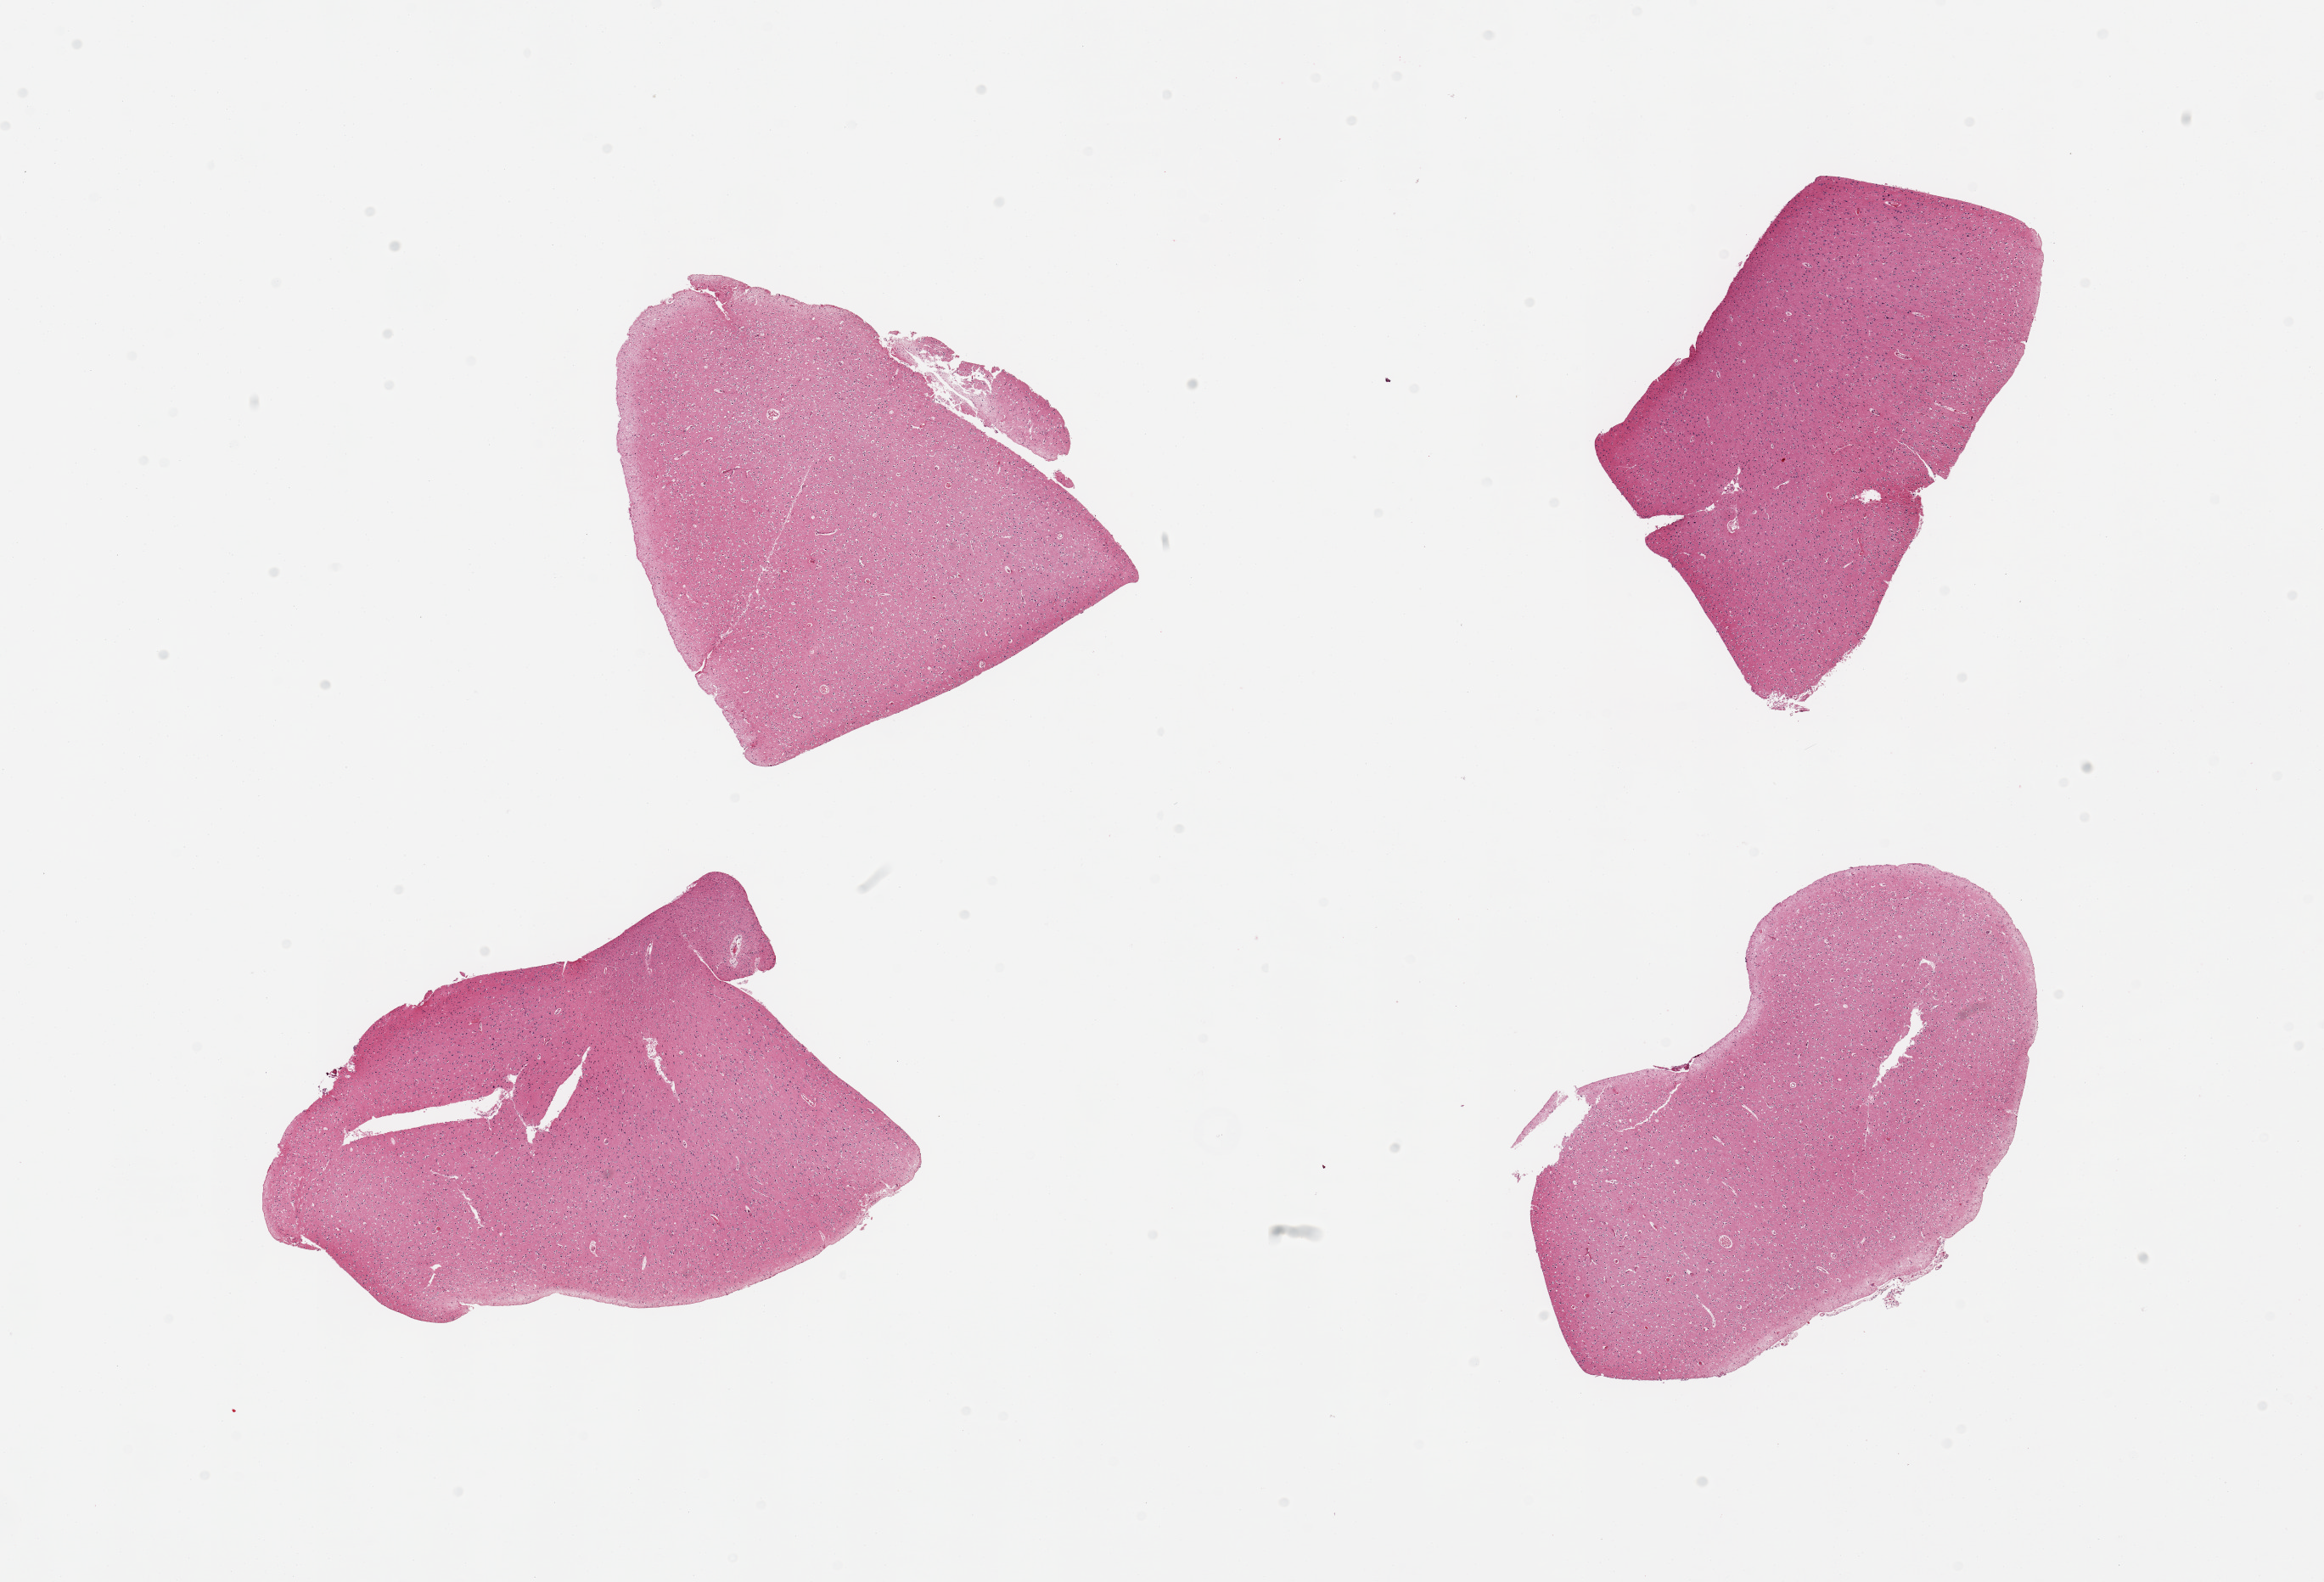
Whole-slide image, haematoxylin and eosin stain — low-resolution overview of the scanned area, about 21.7 x 14.7 mm, PAXgene-fixed paraffin-embedded (PFPE) section, sampled site (target tissue): cerebral cortex, donor tissue sample.
Pathologist's review note for this sample: 4 pieces.